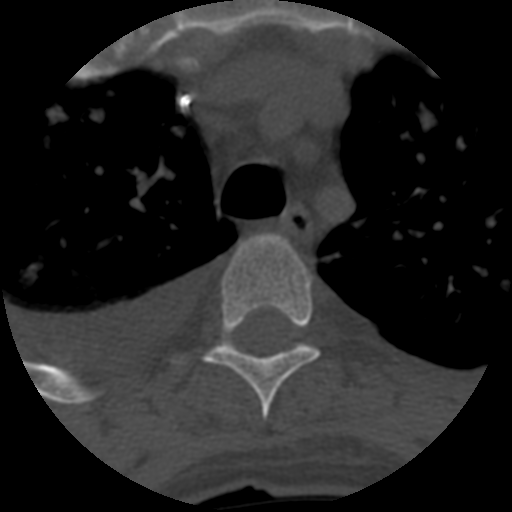
CT including the spine, one axial slice; reconstruction kernel STANDARD; one of 3 acquisitions stored at this slice position; bone window (W 1800 / L 400 HU); 512 × 512 image matrix. Patient age 55 years. Case-level facts recorded for this patient, not image findings: primary cancer: colon.
Structures marked on this image (semi-automatic segmentation, software-assisted and operator-edited):
- T4 vertebra: box from (x=205, y=235) to (x=319, y=421) px